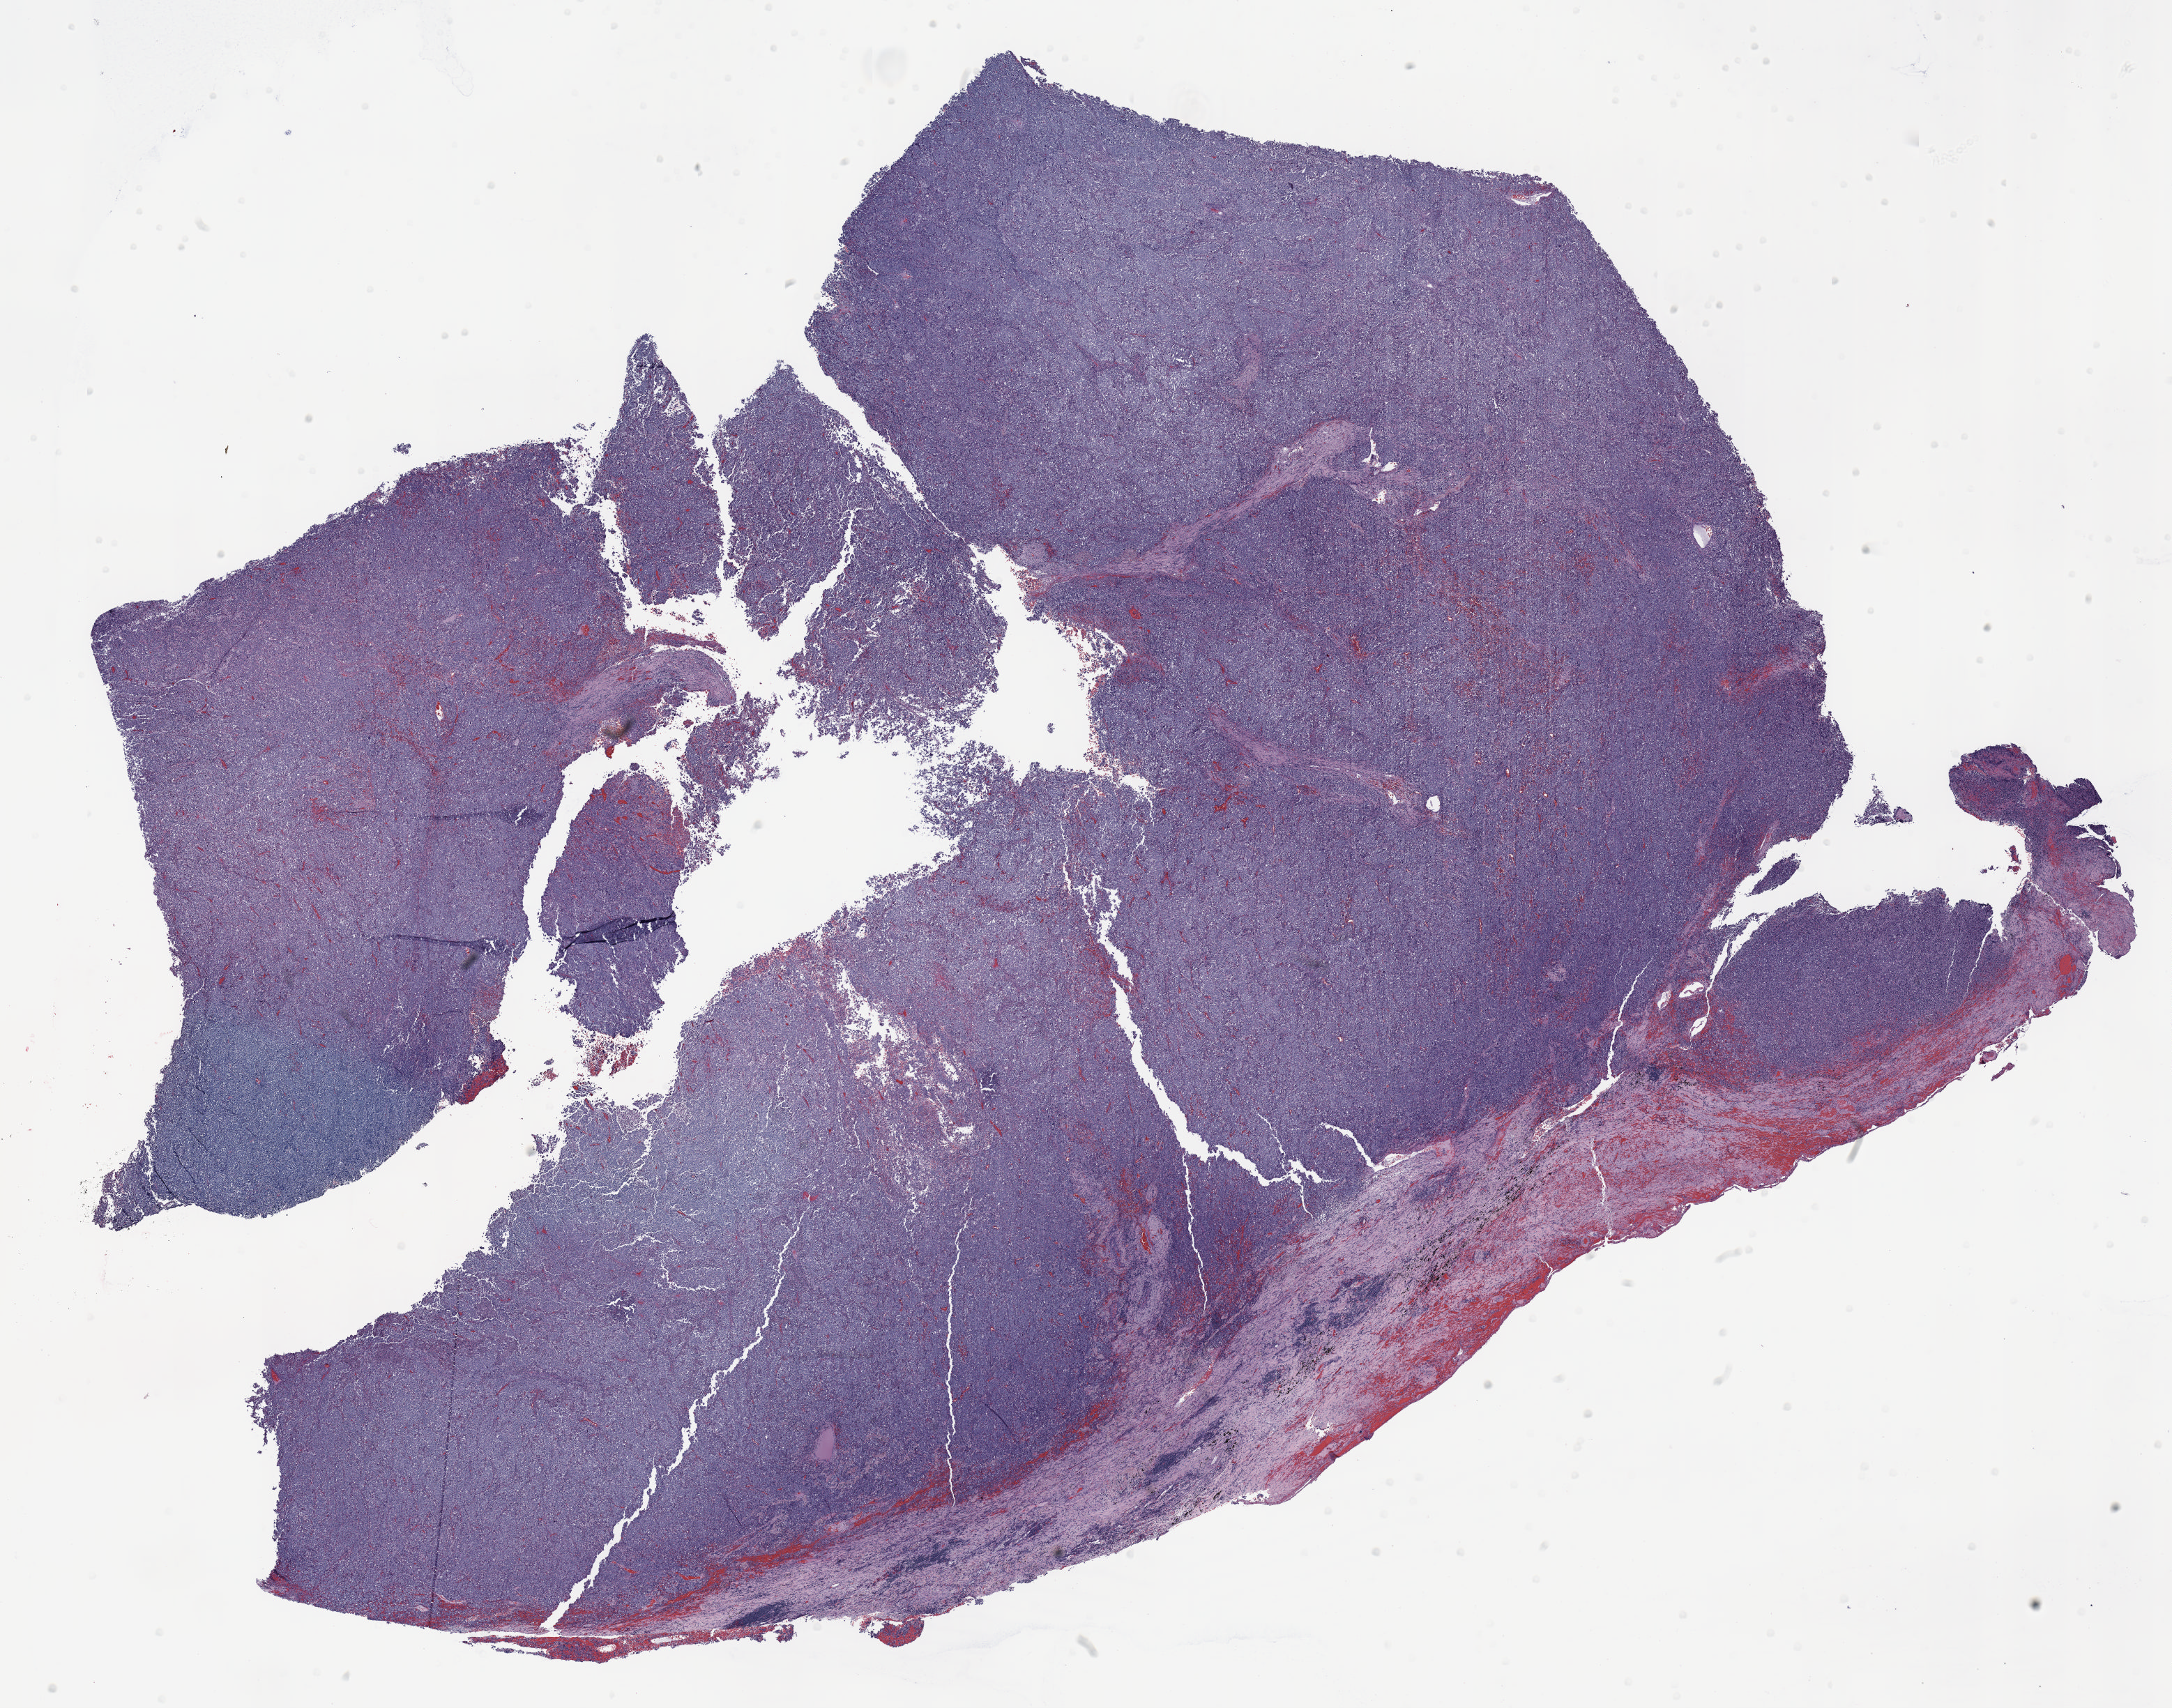
Whole-slide histology image, H&E, low-resolution overview of the scanned area, about 25.0 x 19.7 mm; FFPE section; lung tissue. Male, age 55 at enrolment. Current smoker at enrolment. Grade: poorly differentiated (G3).
Stage (AJCC 6th edition): IIB. Primary tumour location (clinical record): right upper lobe. Participant's lung-cancer diagnosis: Adenocarcinoma, NOS. Tumour size (pathology): 115 mm.